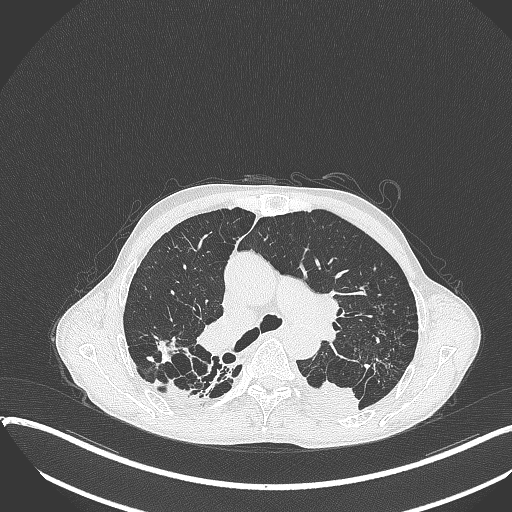
Chest CT, one axial slice; slice 251 of 401 in the series (ordered by position); reconstruction kernel B70f; 120 kVp; lung window (W 1500 / L -600 HU); 1 mm slice thickness; 512 × 512 image matrix, field of view 400 × 400 mm. Patient: male, 57 years. From the clinical record (not read from this slice): clinical TNM (as recorded): T4 N0 M0.
Annotated regions visible in this slice (rectangle marked by the reading radiologist):
- lung tumour (recorded histology: squamous cell carcinoma): bounding box <298,373,362,419> (left, top, right, bottom; pixels)